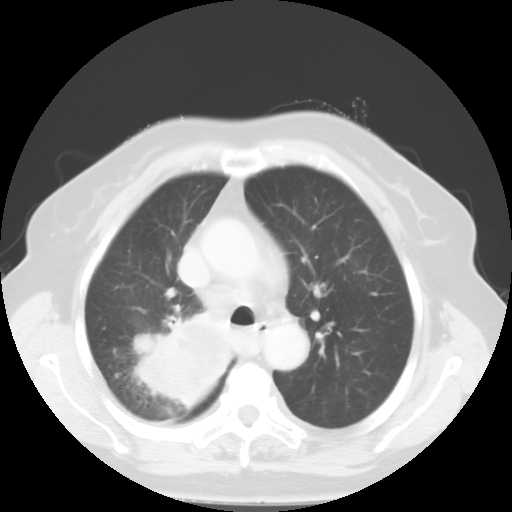
Chest CT, one axial slice. Position 37 of 52 along the scan axis. 120 kVp. Lung window (W 1500 / L -600 HU). 512 × 512 image matrix. Female patient, age 81 years. From the clinical record (not read from this slice): clinical TNM (as recorded): T4 N3 M1b.
Outlined on this slice (bounding box drawn by a radiologist):
- lung tumour (recorded histology: adenocarcinoma): bounding box (x1, y1, x2, y2) in pixels: (132, 307, 236, 412)